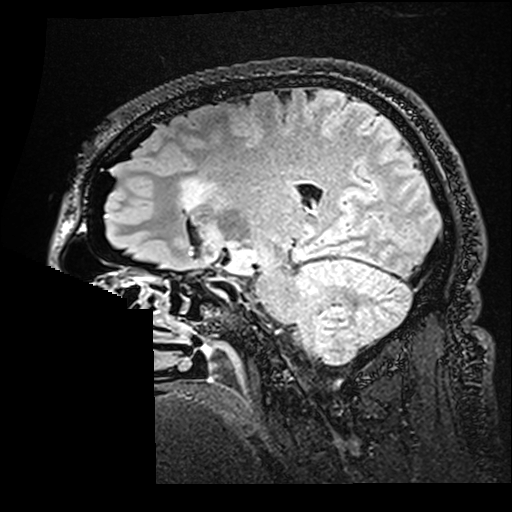
Brain MRI from a brain-tumour surgery series, one sagittal slice. T2 FLAIR. 1 mm slice thickness. 512 × 512 image matrix, field of view 250 × 250 mm. Case-level facts recorded for this patient, not image findings: histopathology: Astrocytoma; WHO grade: 2; IDH mutation: yes.
Annotated regions visible in this slice (manually delineated by an expert):
- residual tumour: bounding box [x1, y1, x2, y2] px = [182, 180, 213, 209]